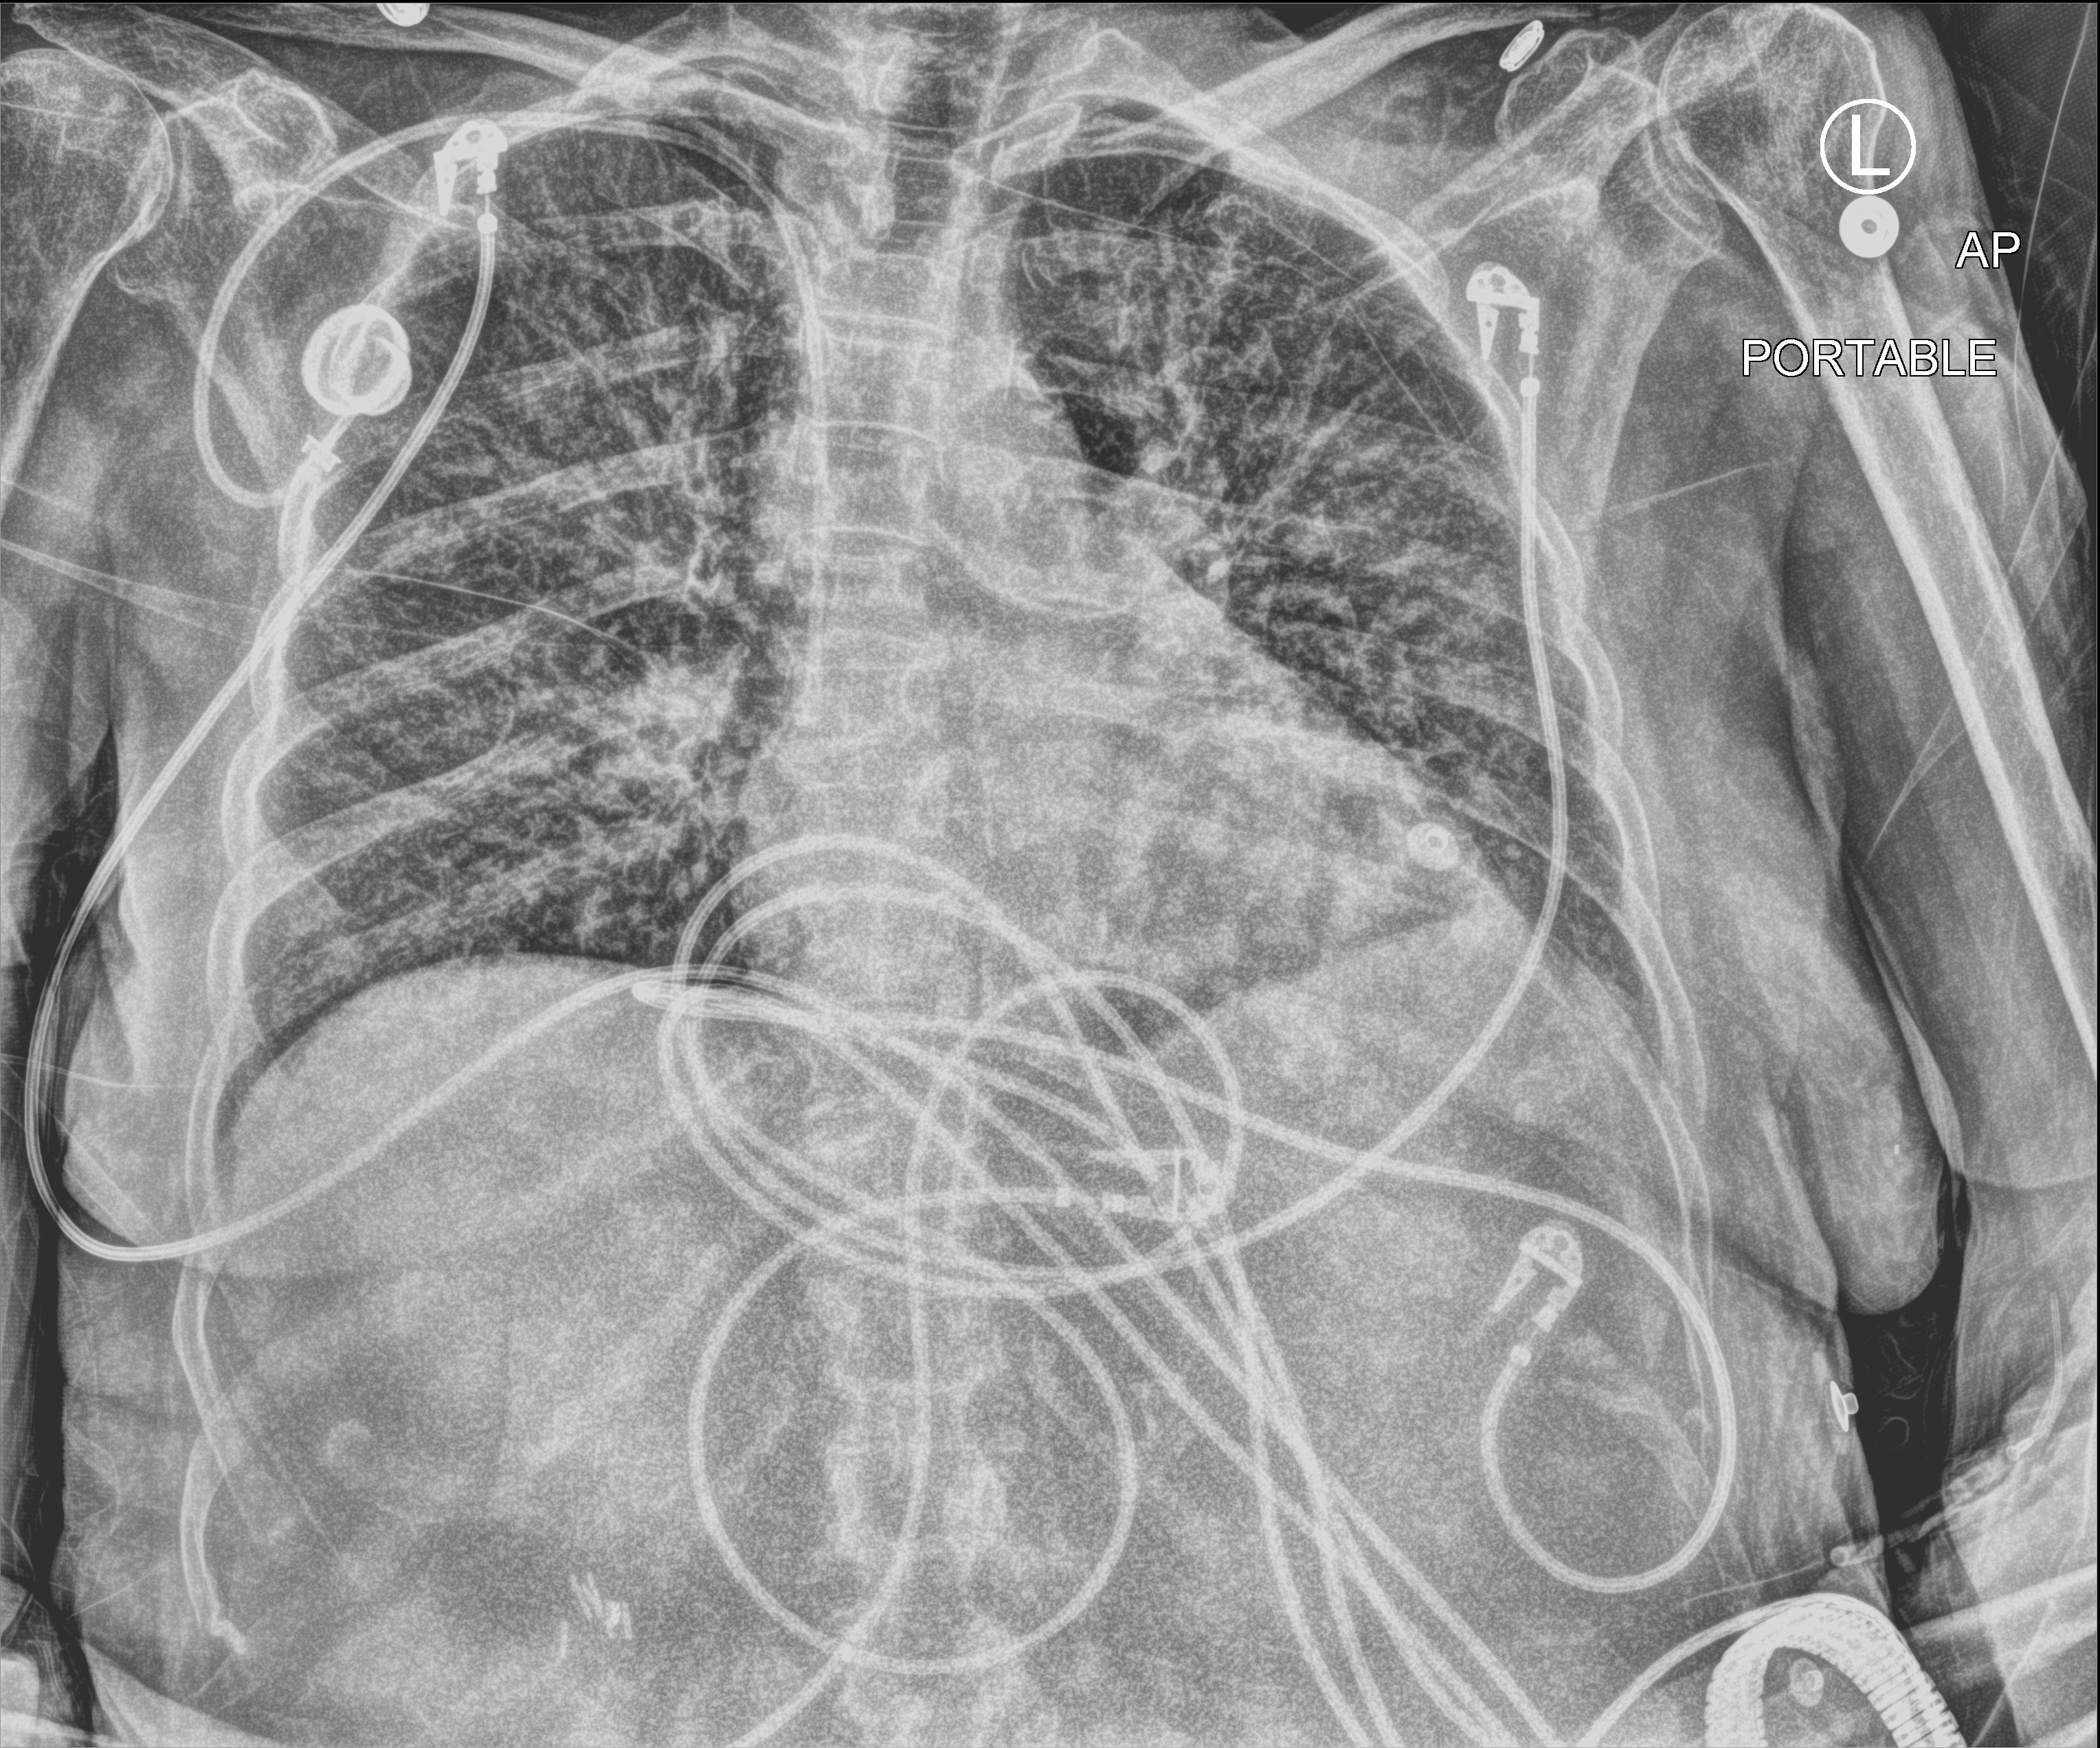
Portable chest radiograph. Patient hospitalised with COVID-19; female, aged 75–90 years.
Hospital-stay facts (about this admission, not read from this image; timing relative to this image not recorded): admitted to intensive care during this hospital stay: yes.